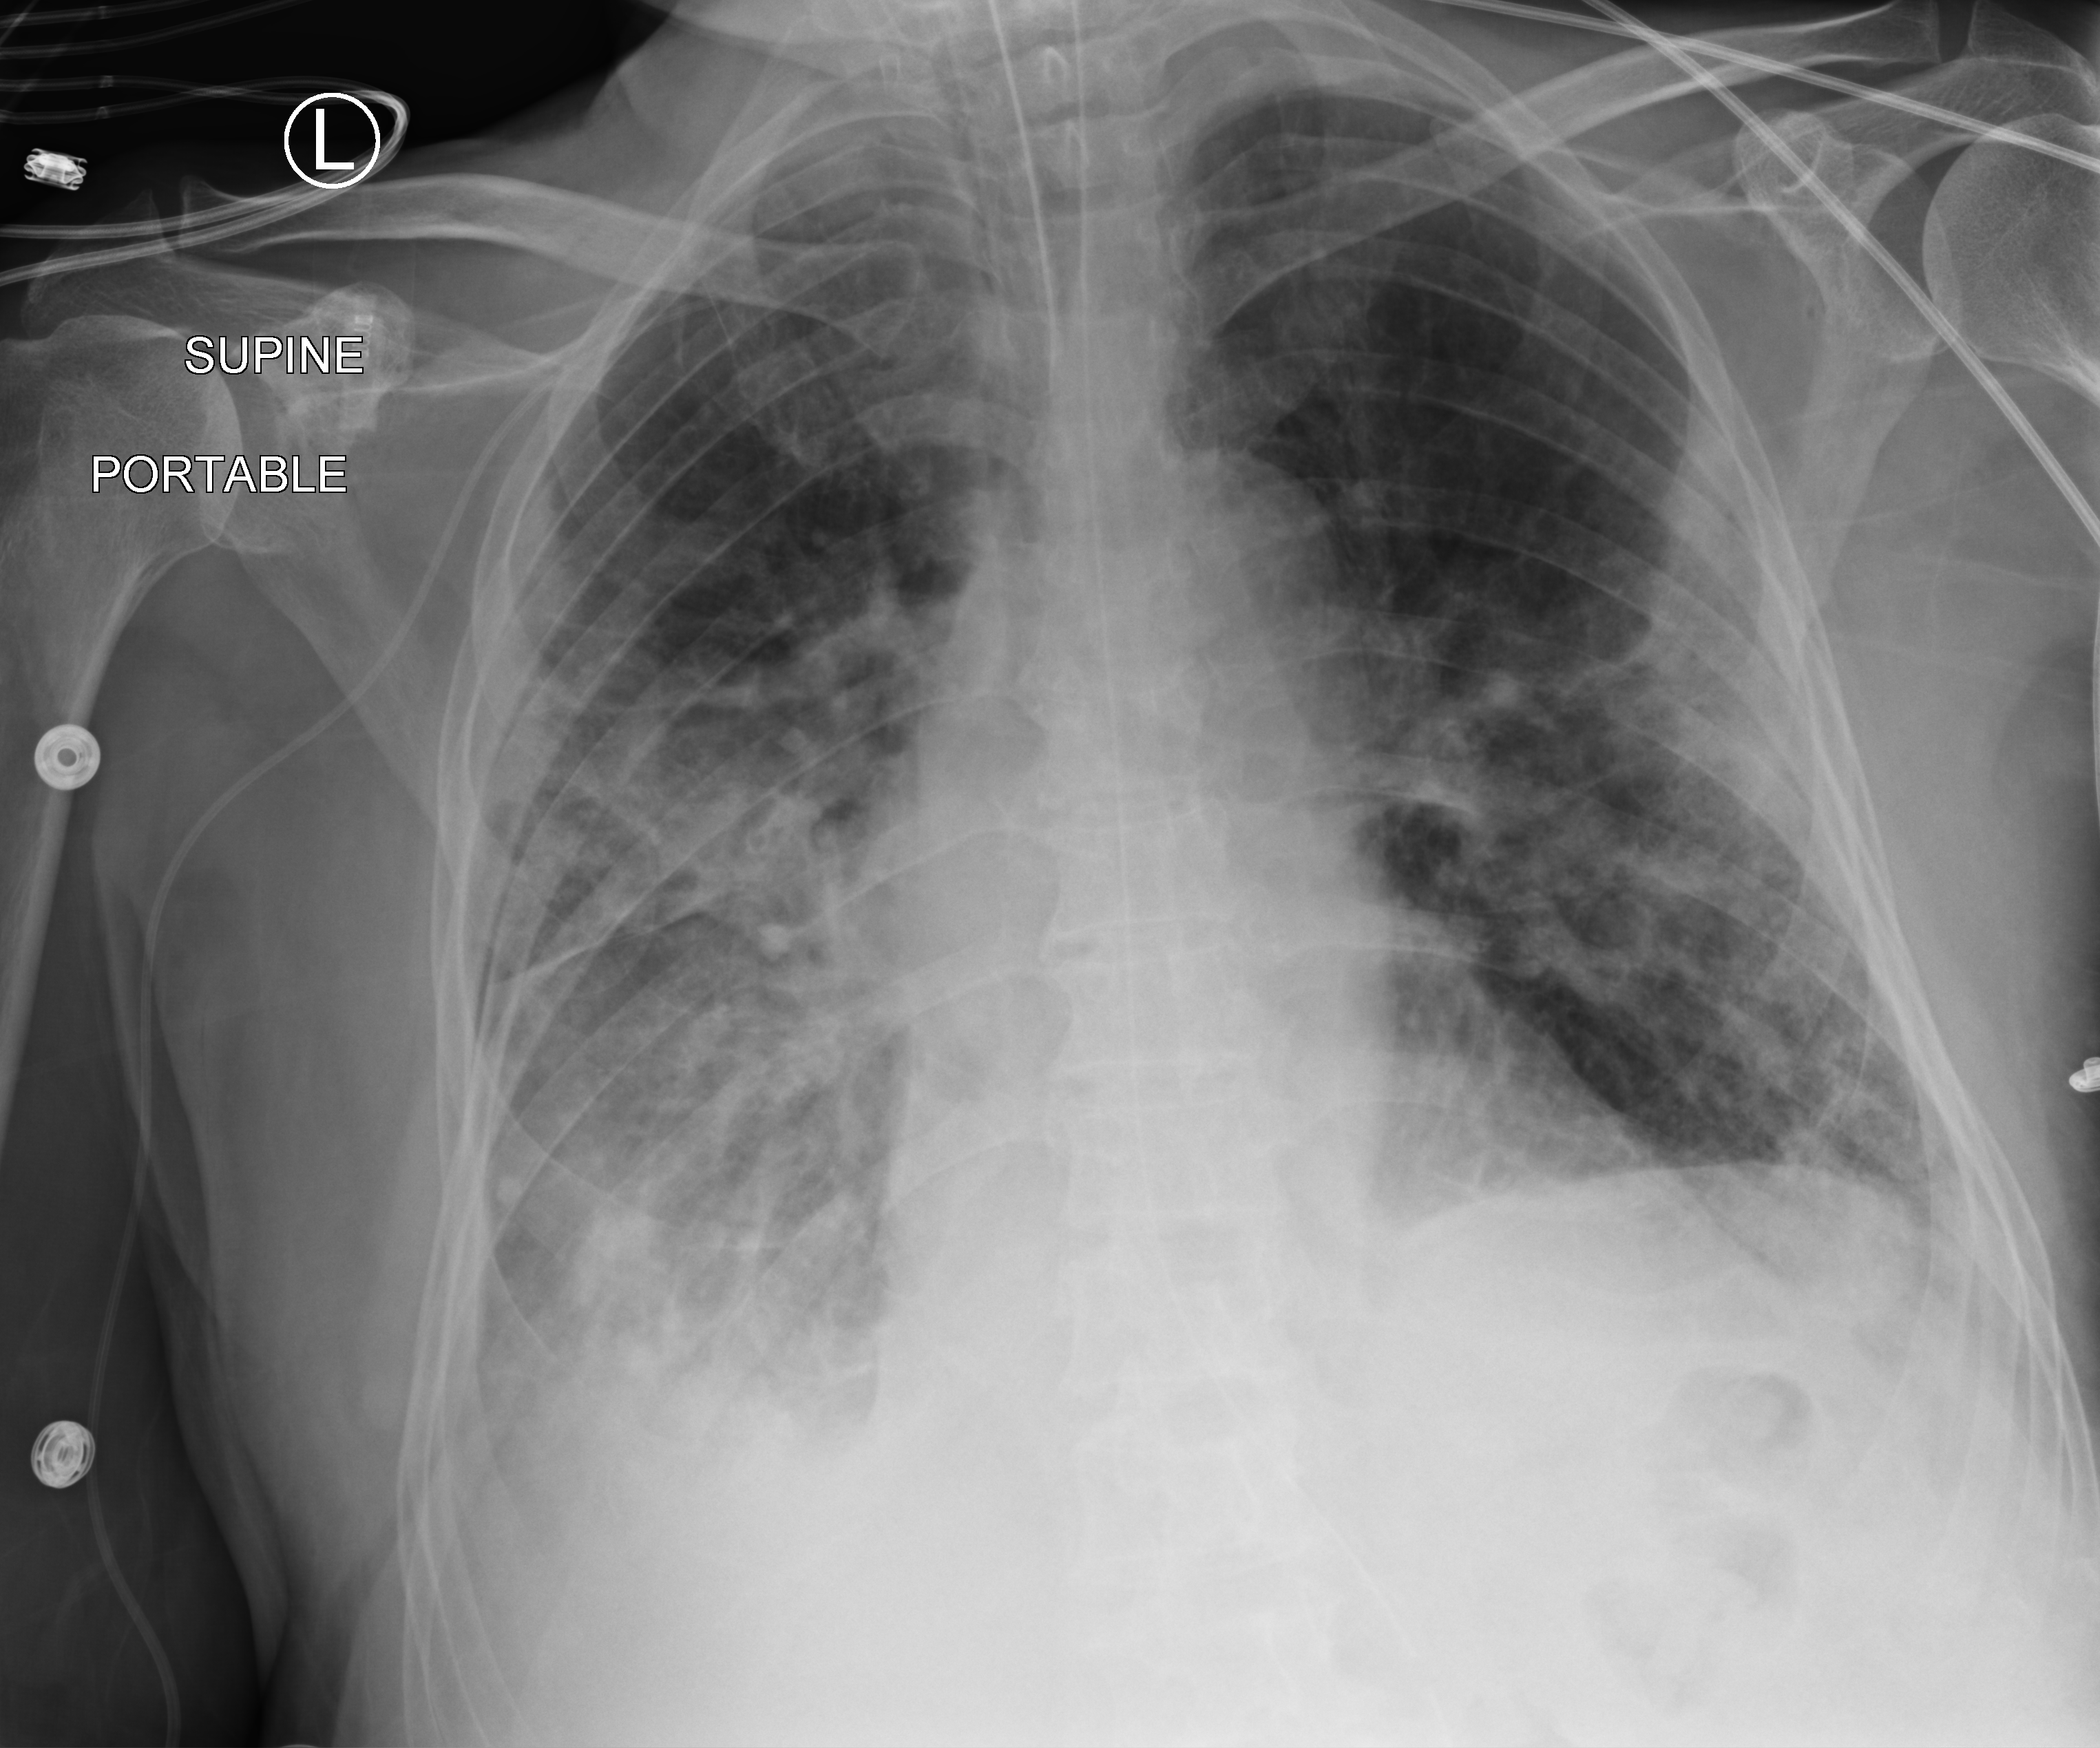
Portable chest radiograph; anteroposterior (AP) projection. Patient hospitalised with COVID-19; male, aged 75–90 years.
Hospital-stay facts (about this admission, not read from this image; timing relative to this image not recorded): COPD (admission record): no; mechanically ventilated during this hospital stay: yes.